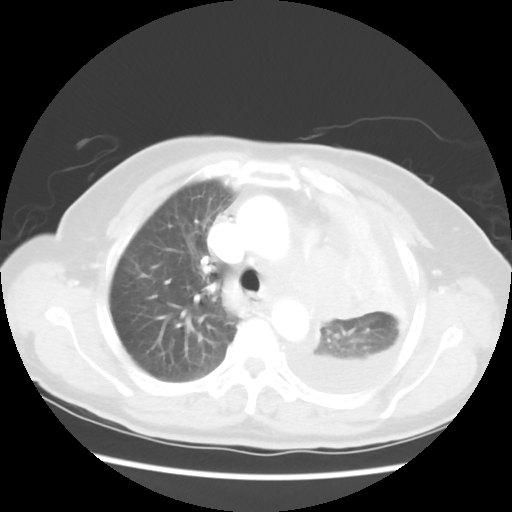
Chest CT, one axial slice. Slice 38 of 52 in the series (ordered by position). Reconstruction kernel STANDARD. 120 kVp. Lung window (W 1500 / L -600 HU). 5 mm slice thickness. 512 × 512 image matrix. Female patient, age 72 years. From the clinical record (not read from this slice): clinical TNM (as recorded): T4 N3 M1b; histopathological grade: G3.
Outlined on this slice (bounding box drawn by a radiologist):
- lung tumour (recorded histology: large cell carcinoma): bounding box [x1, y1, x2, y2] px = [302, 238, 375, 325]